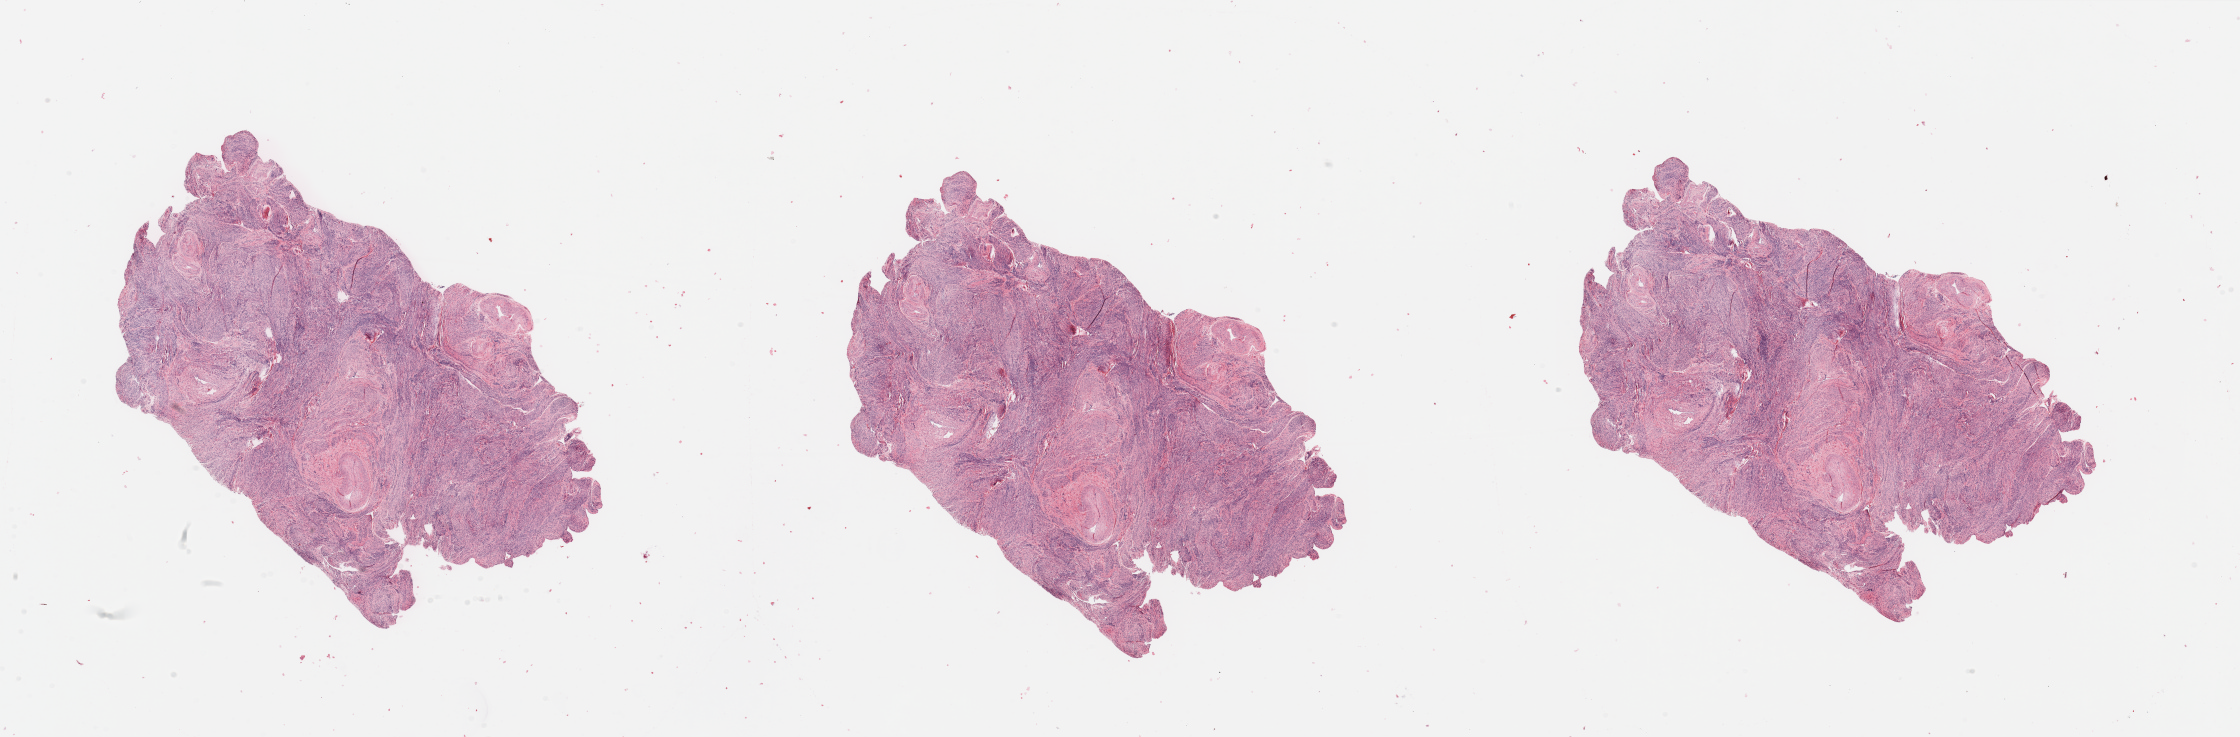
Digitized H&E-stained tissue section (whole slide) — whole scanned area (about 35.4 x 11.7 mm, from a 20x scan) shown as a low-resolution overview, normal (non-tumour) tissue sample, uterus. 53-year-old female patient.
* this section: normal (non-tumour) tissue from the same patient
* patient diagnosis: Endometrioid adenocarcinoma, NOS